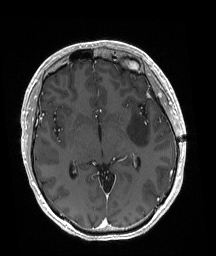
Brain MRI from a brain-tumour surgery series, one axial slice; position 107 of 192 along the scan axis; T1-weighted post-contrast; 1 mm slice thickness; 216 × 256 image matrix, field of view 211 × 250 mm. From the clinical record (not read from this slice): histopathology: Astrocytoma; WHO grade: 3; IDH mutation: yes.
Structures marked on this image (expert manual segmentation):
- tumour: bounding box <128,111,149,147> (left, top, right, bottom; pixels)